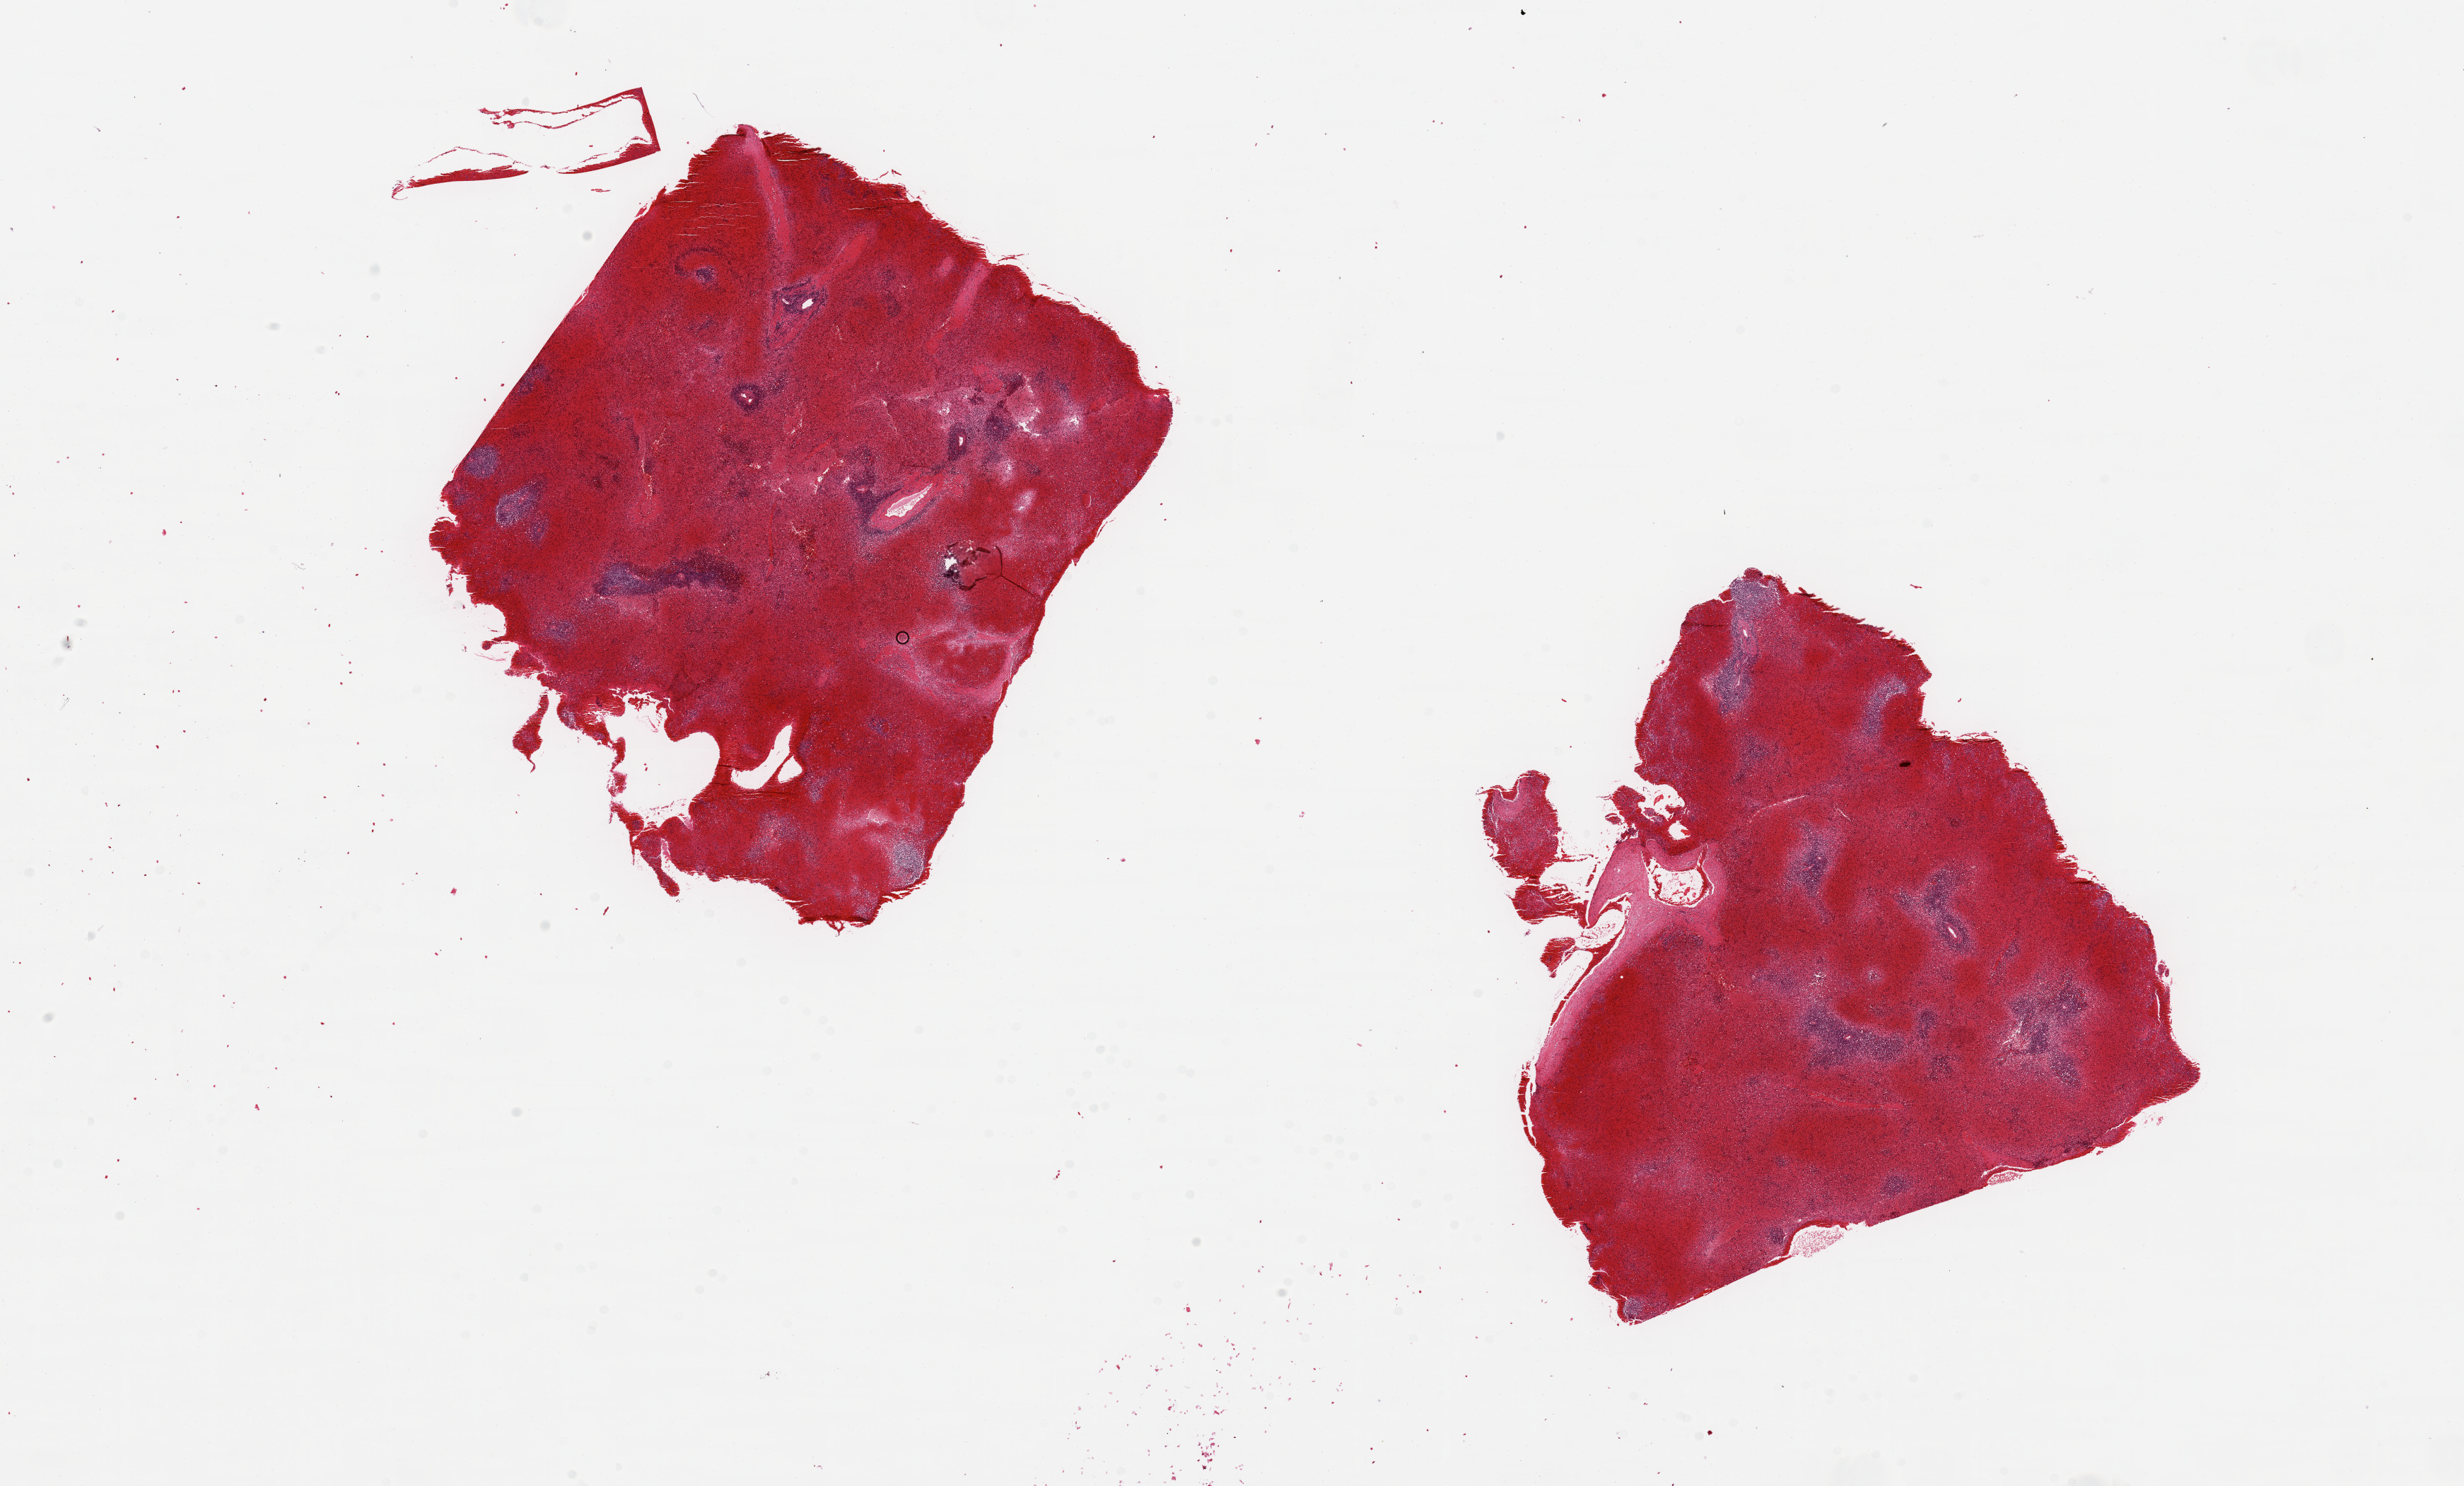
Digitized hematoxylin and eosin (H&E)-stained section, a low-resolution overview of the entire scanned area, about 27.6 x 16.6 mm, PAXgene-fixed paraffin-embedded (PFPE) section, sampled site (target tissue): spleen, donor tissue sample. Female donor.
* reviewer comment on this tissue sample: 2 pieces, 9x8 & 7x7mm; Severe congestion